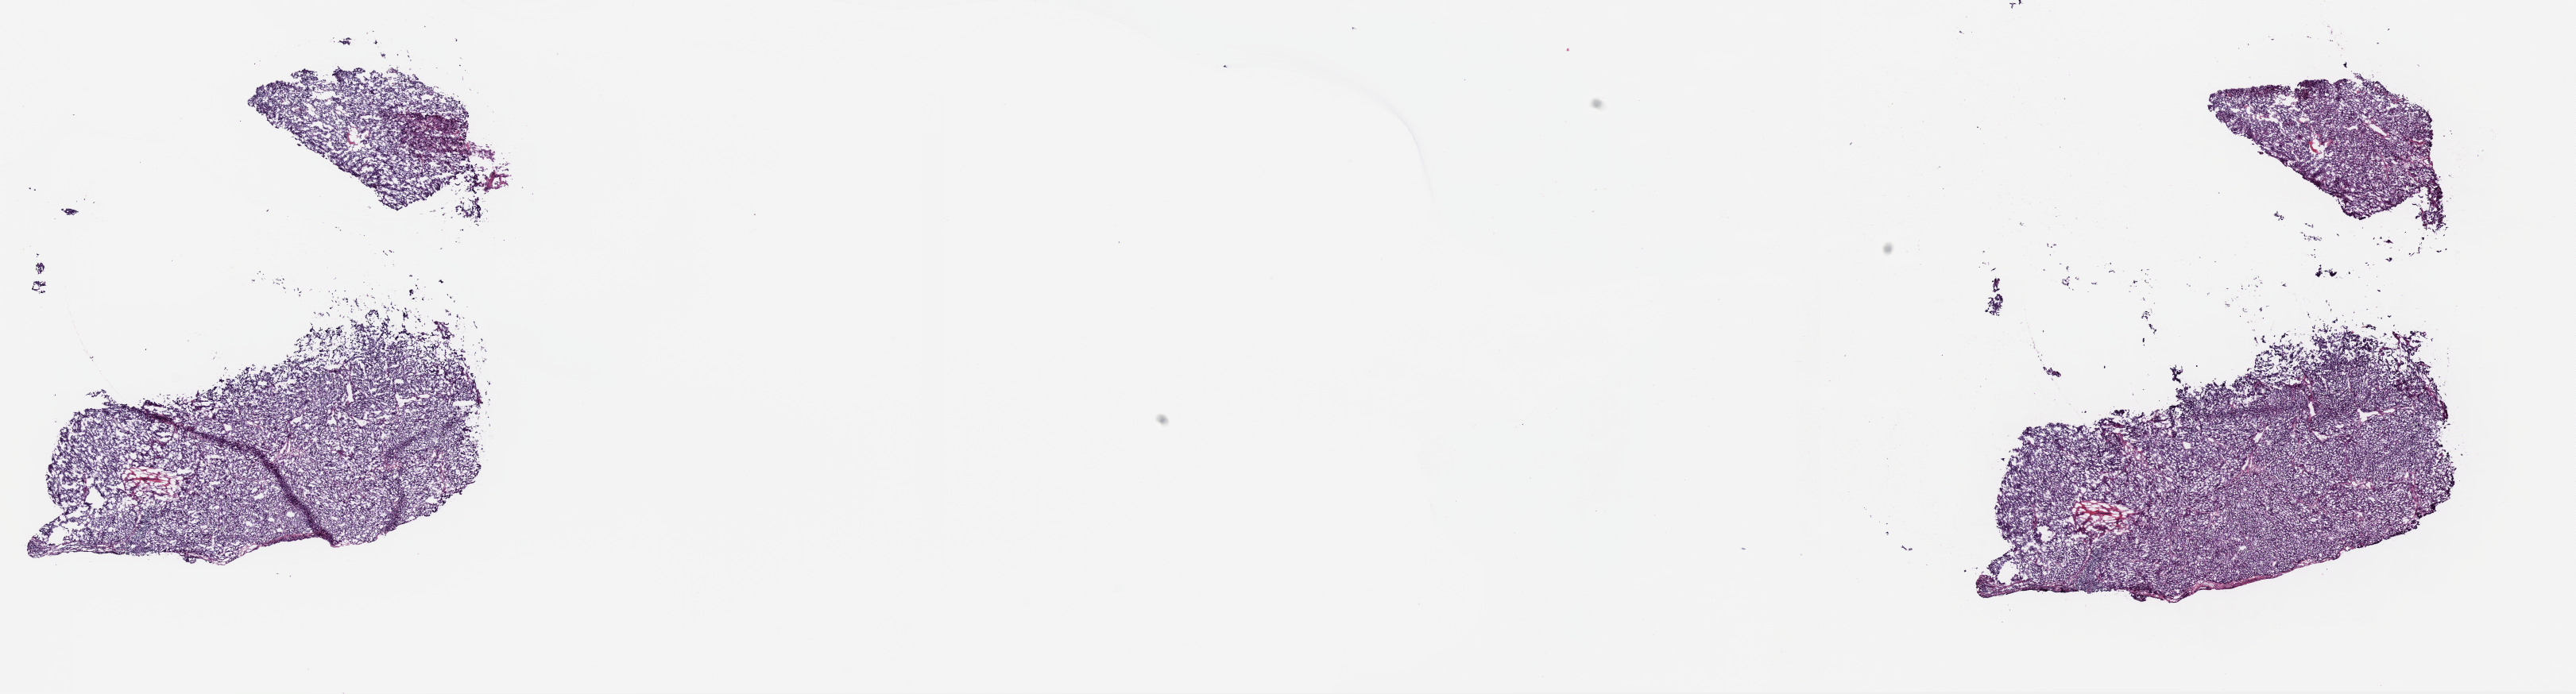
Digitized Hematoxylin and eosin (H&E) stained tissue section (whole slide), whole scanned area (about 25.6 x 6.9 mm, slide scanned at 40x) shown as a low-resolution overview; frozen section from the top of the tissue portion; metastatic tumour sample, sampled site not recorded. Male patient; age at initial diagnosis 50 years. Composition of this section per pathologist review: tumour cells 100%, tumour nuclei 97%, normal cells 0%, stromal cells 0%, necrosis 0%. Infiltration values recorded for this section: lymphocyte infiltration 0%, monocyte infiltration 0%, neutrophil infiltration 0%.
* this section: metastatic tumour tissue
* patient diagnosis: Malignant melanoma, NOS